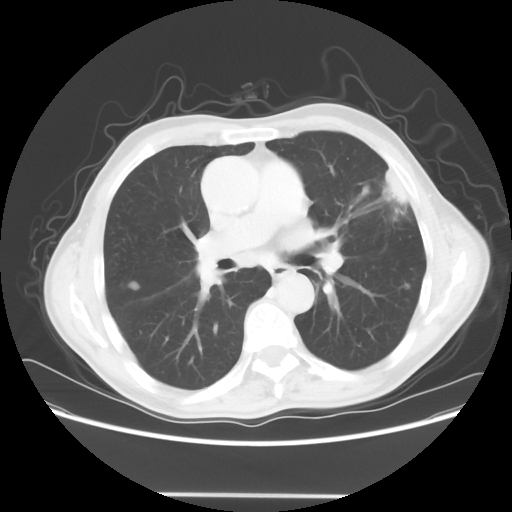
Chest CT, one axial slice. Reconstruction kernel STANDARD. 120 kVp. Lung window (W 1500 / L -600 HU). 5 mm slice thickness. 512 × 512 image matrix, field of view 392 × 392 mm. Patient: male, 71 years. From the clinical record (not read from this slice): clinical TNM (as recorded): T1c N0 M0; histopathological grade: G2-3.
Structures marked on this image (rectangle marked by the reading radiologist):
- lung tumour (recorded histology: adenocarcinoma): bounding box [x1, y1, x2, y2] px = [366, 152, 410, 209]